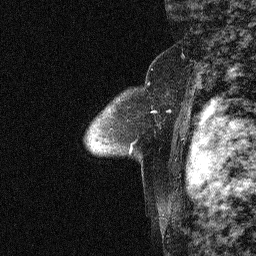
Breast MRI (dynamic contrast-enhanced), one sagittal slice. Slice 48 of 64 in the series (ordered by position). Dynamic contrast-enhanced study with each time point stored as its own series, time point 2 of 3 at this slice position (early post-contrast, ordered by acquisition time). 1.5 T. TE 4.5 ms, TR 11 ms. 256 × 256 image matrix. Patient: female, 46 years. Case-level facts recorded for this patient, not image findings: setting: breast cancer imaged before/during neoadjuvant chemotherapy; receptor status: HER2-positive.
Annotated regions visible in this slice (semi-automatic segmentation, software-assisted and operator-edited):
- analysis volume of interest (the breast-tissue region the enhancement analysis was run in; not a lesion): bounding box (x1, y1, x2, y2) in pixels: (46, 51, 180, 169)
- tumour enhancement mask (voxels above the 90 % enhancement threshold inside the analysis volume of interest): (153, 110, 170, 113)